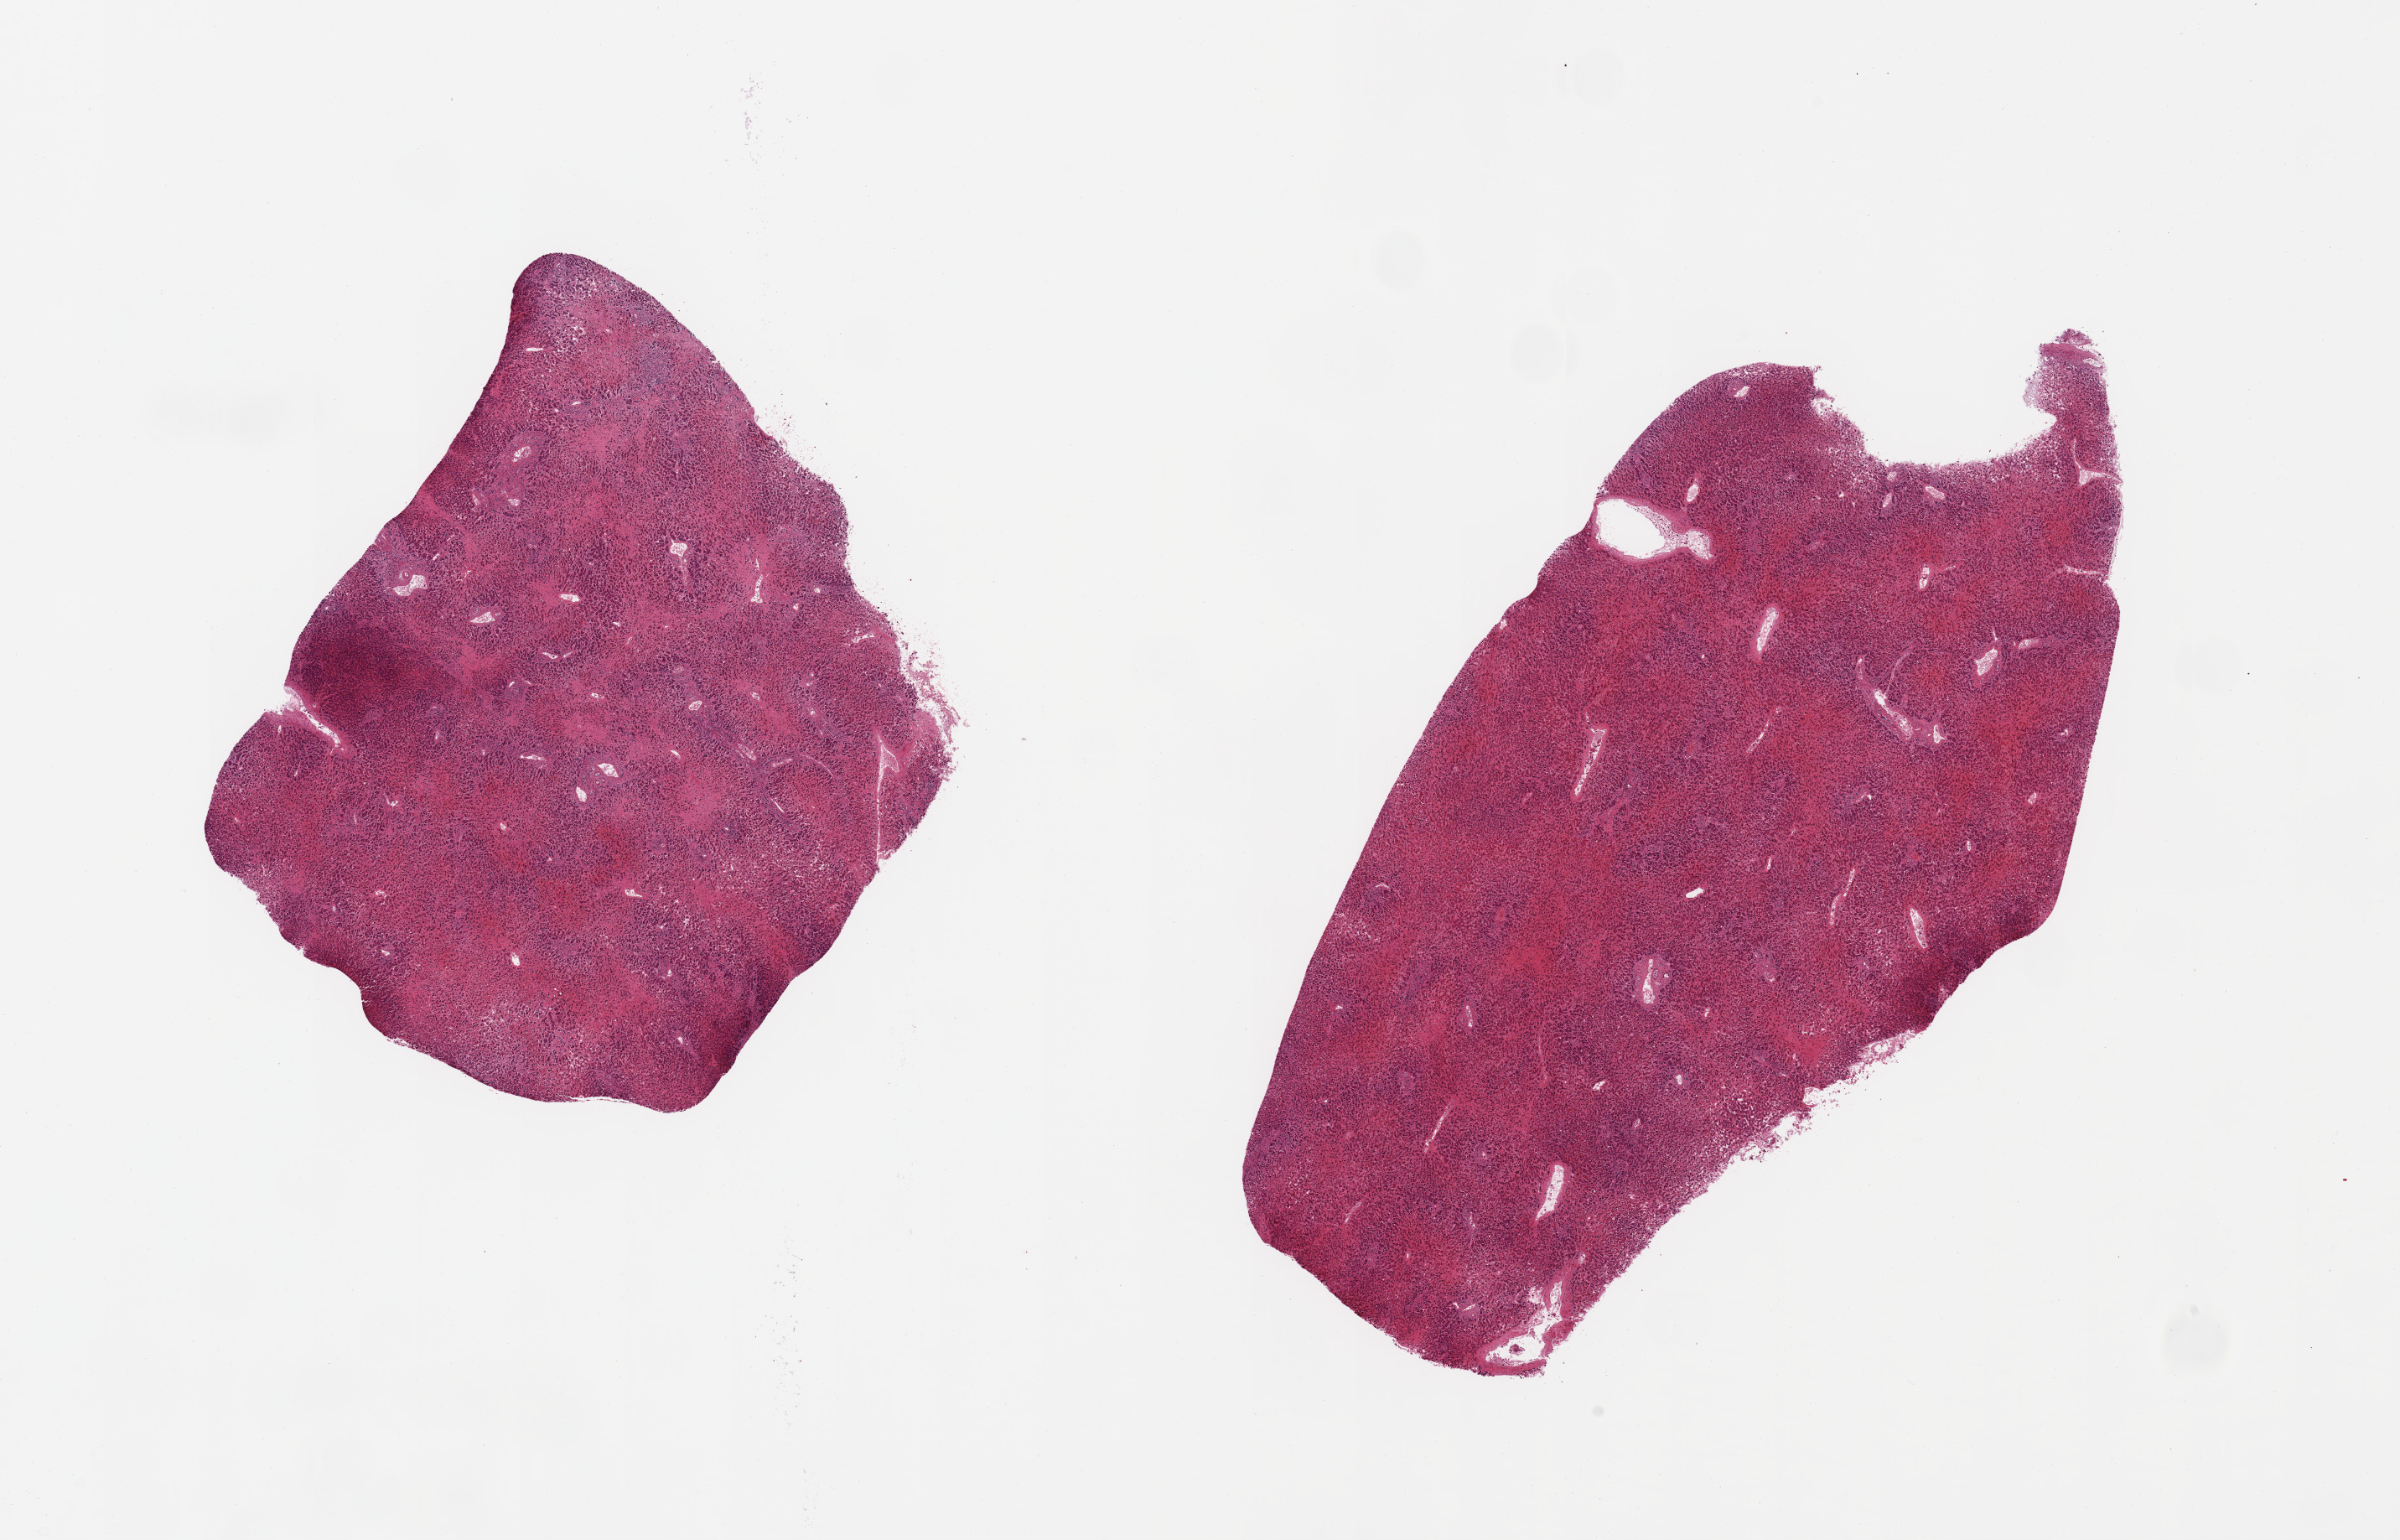
Haematoxylin and eosin whole-slide image, whole scanned area (about 22.6 x 14.5 mm) shown as a low-resolution overview, PAXgene-fixed paraffin-embedded (PFPE) section, sampled site (target tissue): liver, tissue donor sample.
Pathologist's review note for this sample: 2 pieces, advanced chronic congestion/'cardiac' cirrhosis.